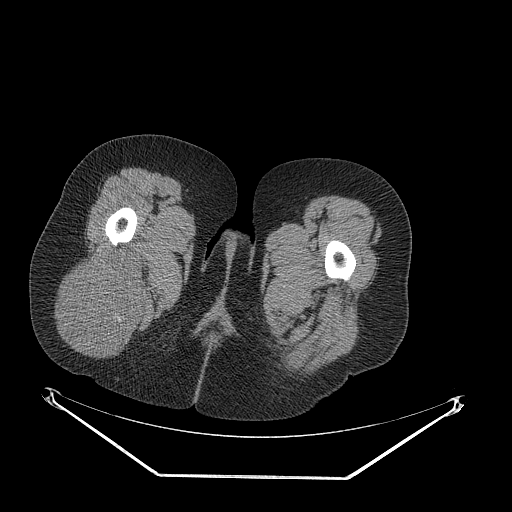
CT of an extremity soft-tissue mass (from a PET/CT study), one axial slice; slice 46 of 257 in the series (ordered by position); reconstruction kernel STANDARD; 140 kVp; soft-tissue window (W 400 / L 40 HU); 3.75 mm slice thickness; 512 × 512 image matrix, field of view 500 × 500 mm. Female patient. Case-level facts recorded for this patient, not image findings: histological type: synovial sarcoma; grade: intermediate; site of the primary tumour: right buttock.
Outlined on this slice (expert contour drawn on MRI and transferred to this co-registered scan by the dataset authors):
- gross tumour volume including surrounding oedema: bounding box [x1, y1, x2, y2] px = [64, 249, 147, 350]
- gross tumour volume (mass): [64, 249, 147, 350]